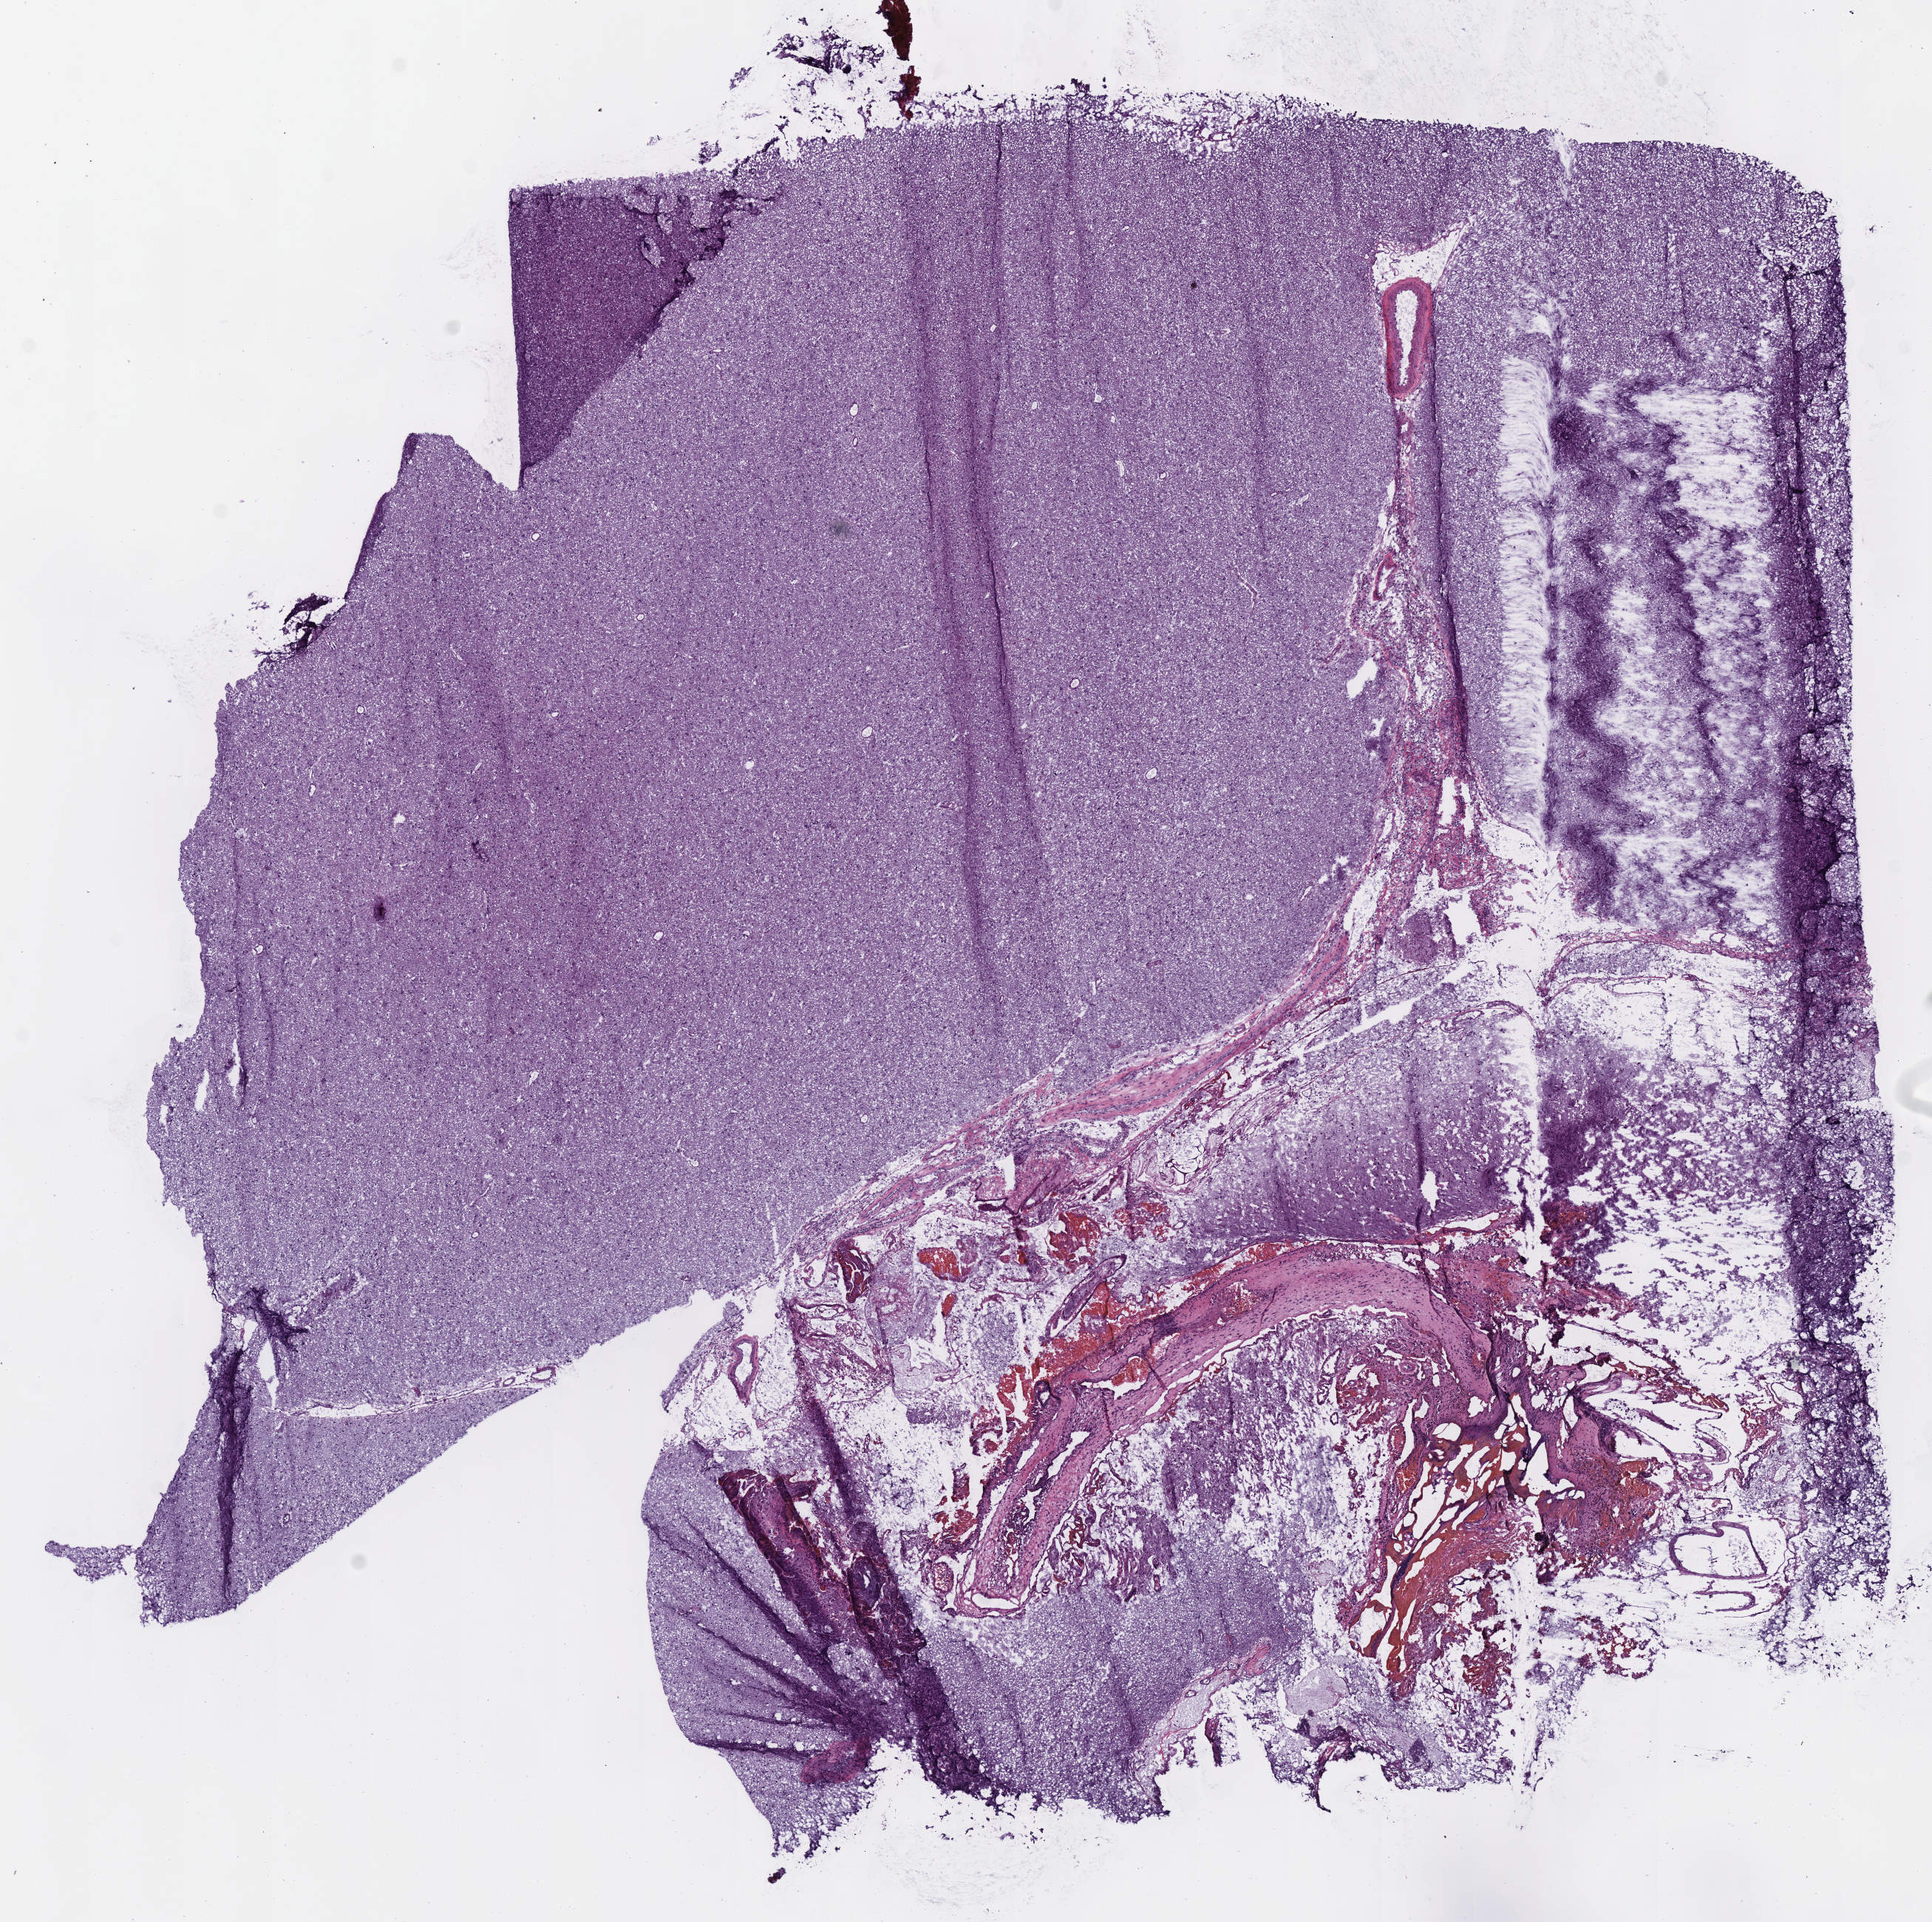
Whole-slide histology image, Hematoxylin and eosin (H&E) stained, shown as a low-resolution overview of the whole scanned area (about 10.3 x 10.2 mm, slide scanned at 40x). Frozen section from the bottom of the tissue portion. Sample: primary tumour, brain. Female, age 40 years at initial diagnosis. Histologic grade: G2 (moderately differentiated). Pathologist review of this section (percent, as recorded): tumour cells 100%, tumour nuclei 50%, normal cells 0%, stromal cells 0%, necrosis 0%.
Pathologic diagnosis: Mixed glioma (cerebrum).